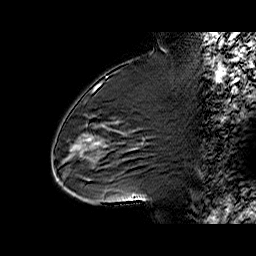
Breast MRI (dynamic contrast-enhanced), one sagittal slice. Position 33 of 60 along the scan axis. Dynamic contrast-enhanced series, time point 2 of 6 at this slice position (early post-contrast). 1.5 T. TE 6.3 ms, TR 32.4 ms. 4 mm slice thickness. 256 × 256 image matrix, field of view 200 × 200 mm. Female patient. Case-level facts recorded for this patient, not image findings: setting: breast cancer imaged before/during neoadjuvant chemotherapy; receptor status: triple-negative.
Outlined on this slice (semi-automatic segmentation, software-assisted and operator-edited):
- analysis volume of interest (the breast-tissue region the enhancement analysis was run in; not a lesion): bounding box <65,88,138,187> (left, top, right, bottom; pixels)
- tumour enhancement mask (voxels above the 100 % enhancement threshold inside the analysis volume of interest): <87,137,97,145>